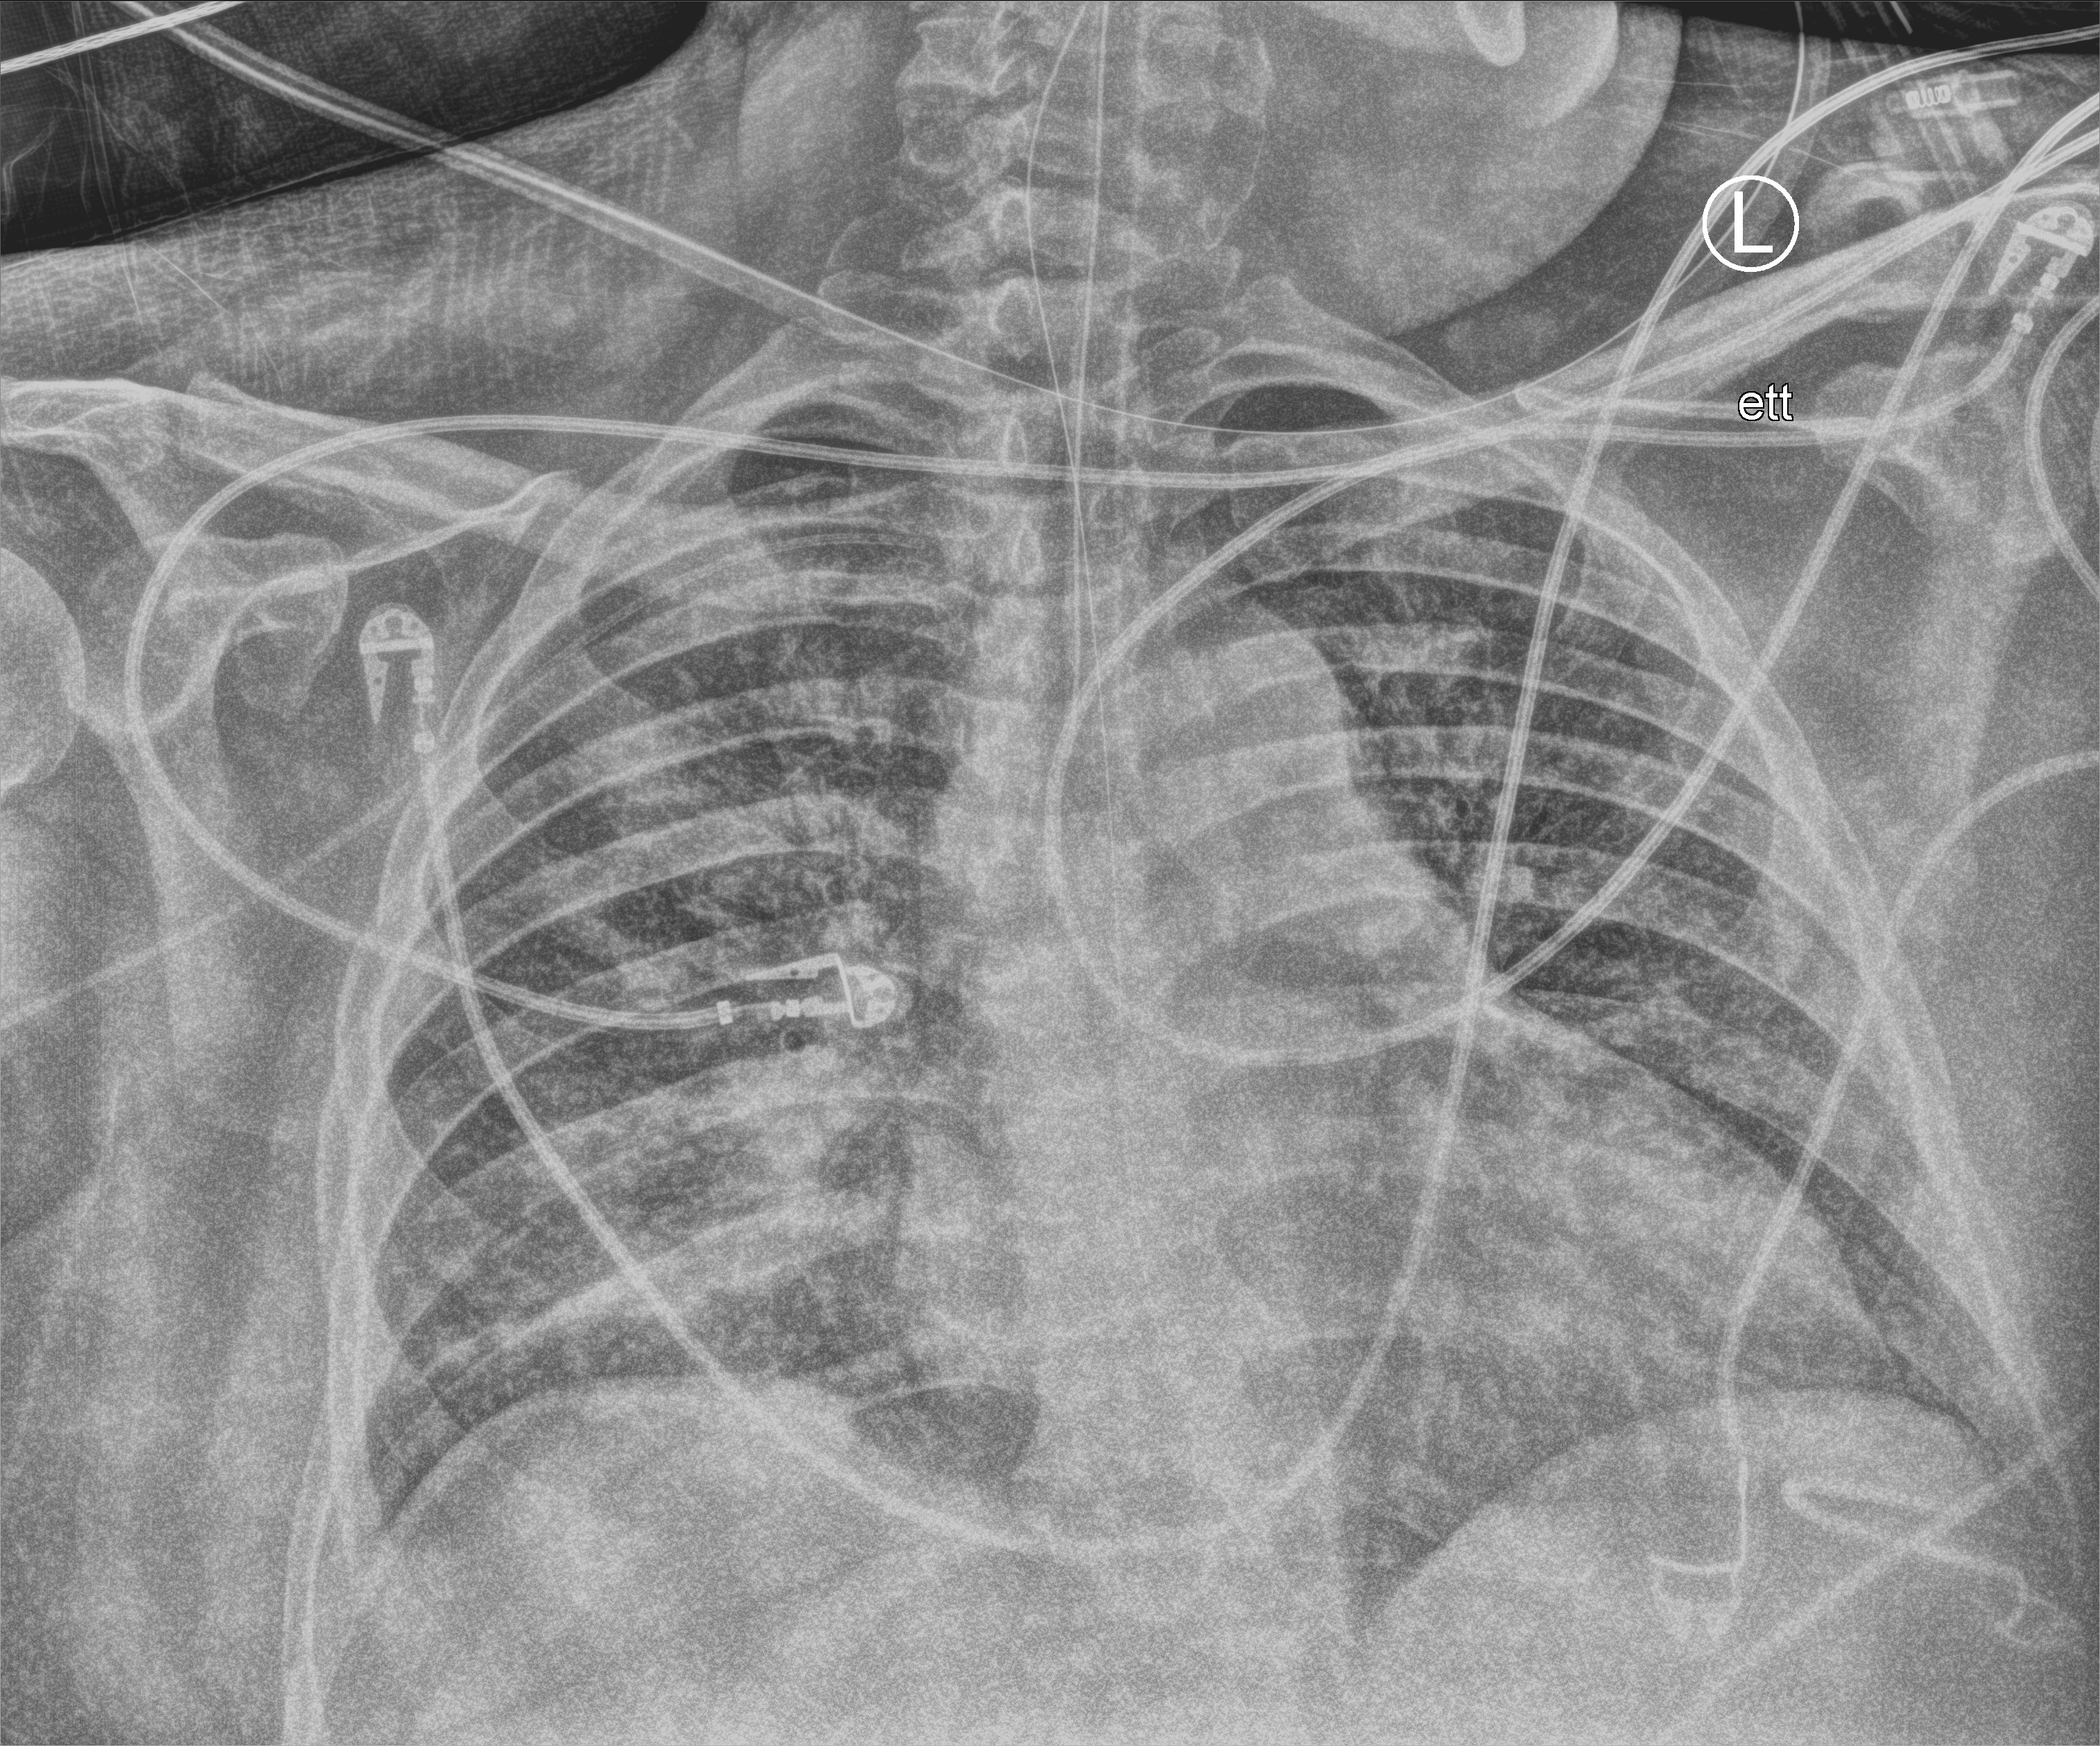
Chest X-ray (portable), anteroposterior (AP) projection. Male patient hospitalised with COVID-19, age 18–59 years.
Admission-level facts for this patient (not findings on this image; timing relative to this image not recorded): smoking status (admission record): never.